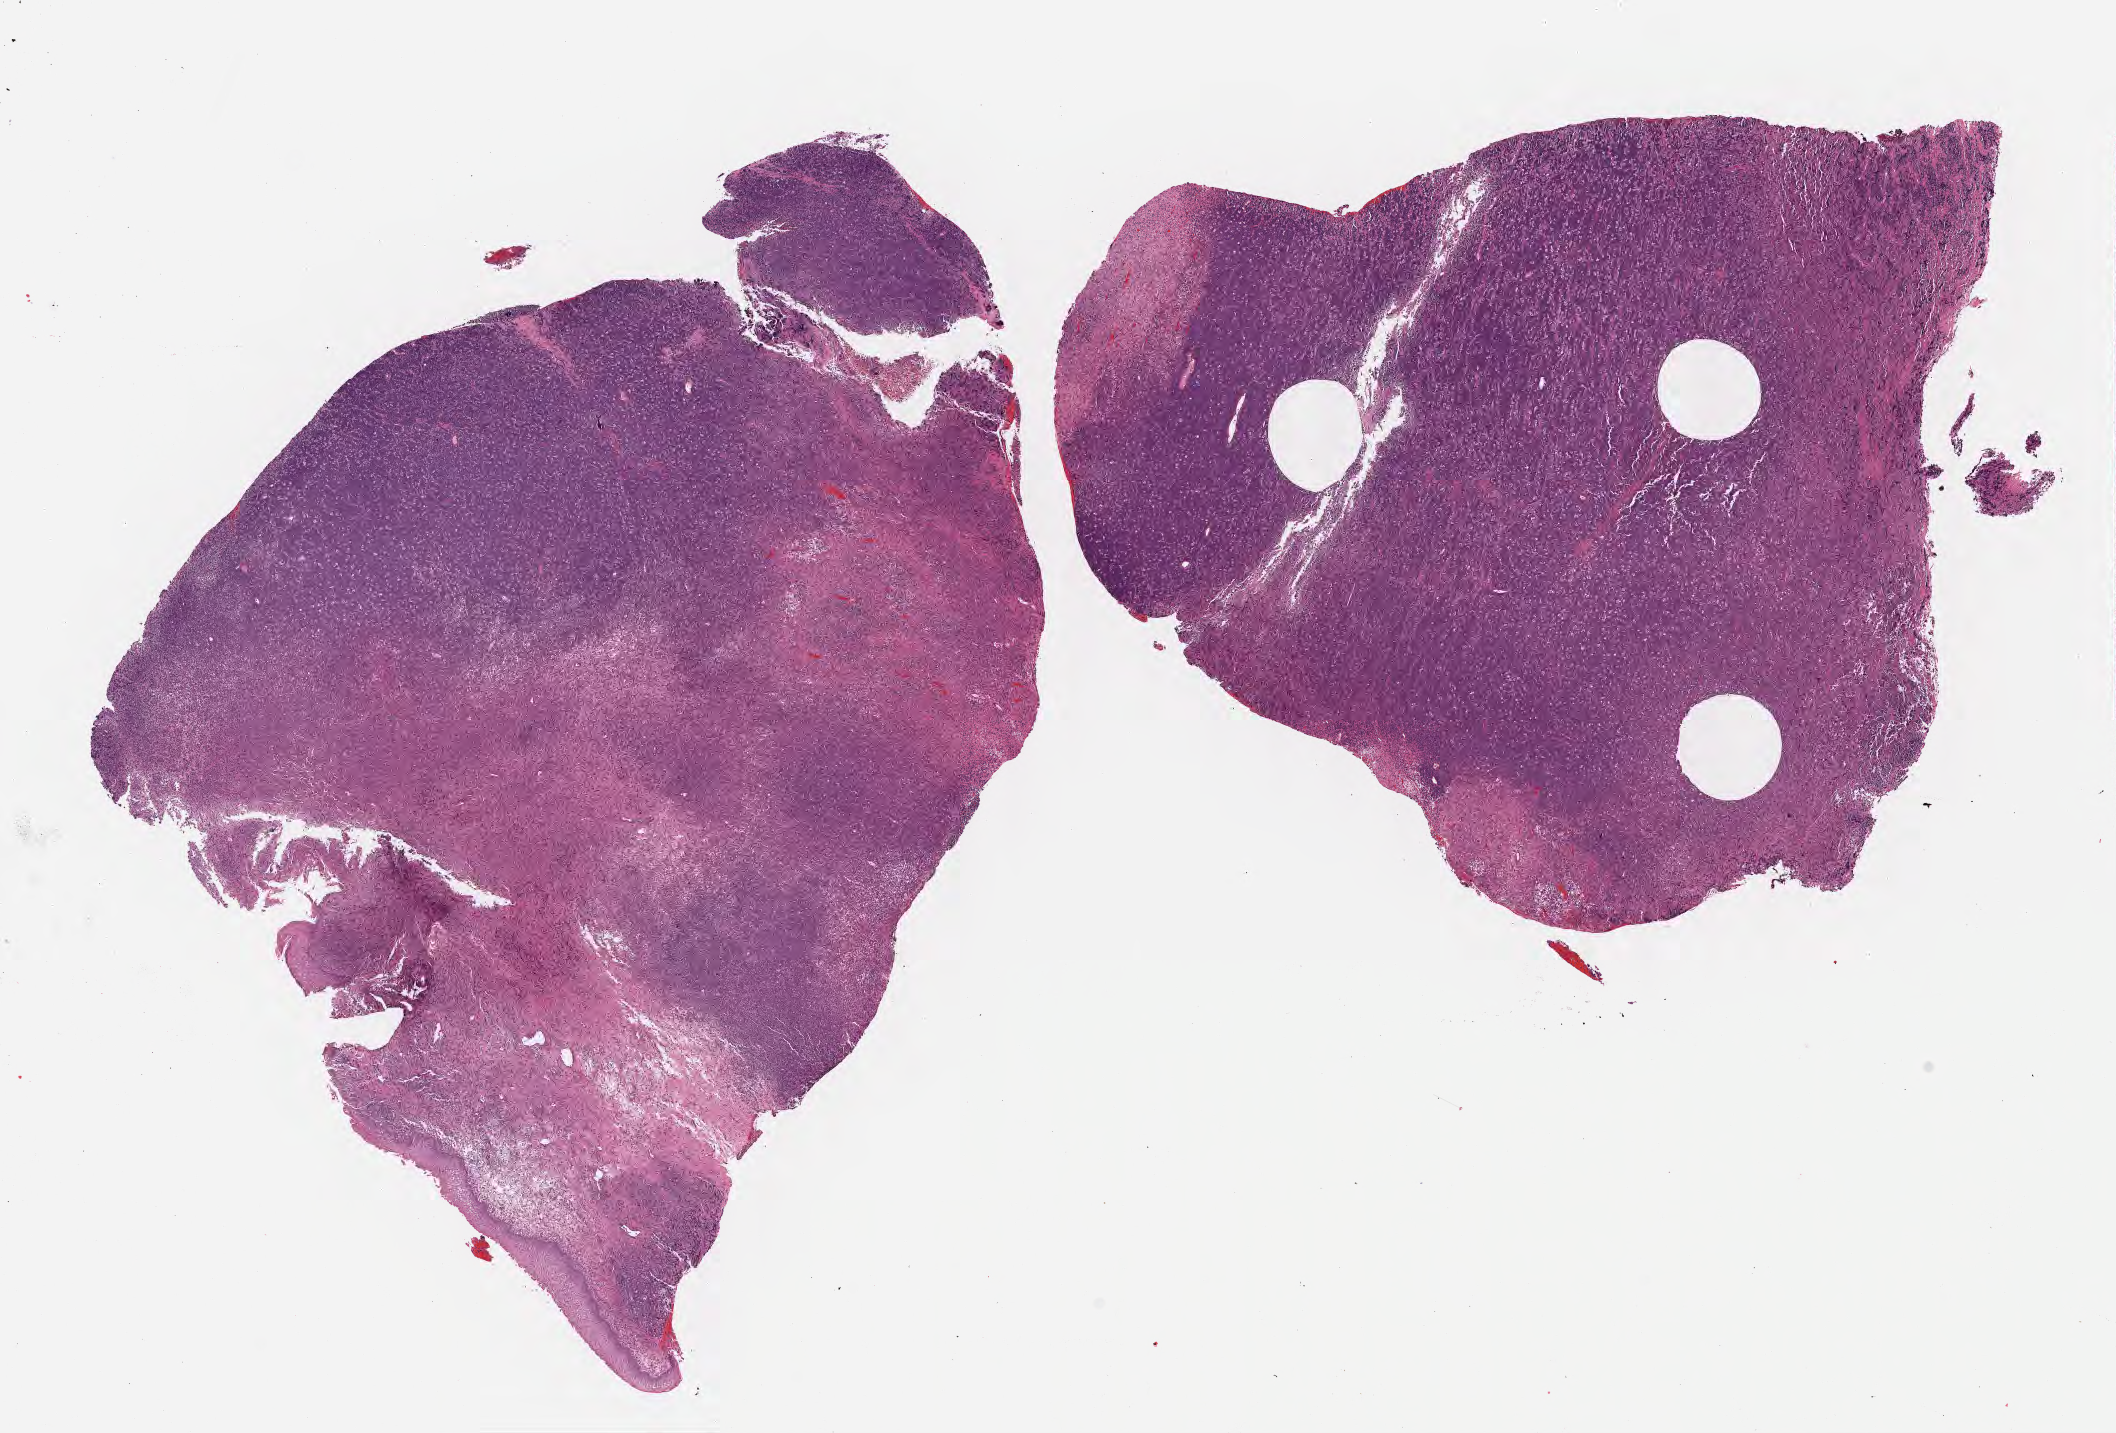
Digitized haematoxylin and eosin-stained section — shown as a low-resolution overview of the whole scanned area (about 17.1 x 11.6 mm), formalin-fixed paraffin-embedded section, primary tumor, anatomic site: mandible. Patient: male, age at initial diagnosis 6 years. Pathologist review of this section (percent, as recorded): tumor cells 60%, tumor nuclei 80%, stromal cells 5%, necrosis 30%, normal cells 5%. Infiltration values recorded for this section: lymphocyte infiltration 30%, monocyte infiltration 40%, neutrophil infiltration 5%.
• Ann Arbor stage (patient): Stage IV
• section: bottom of the tissue portion
• histologic diagnosis: Diffuse large B-cell lymphoma, NOS